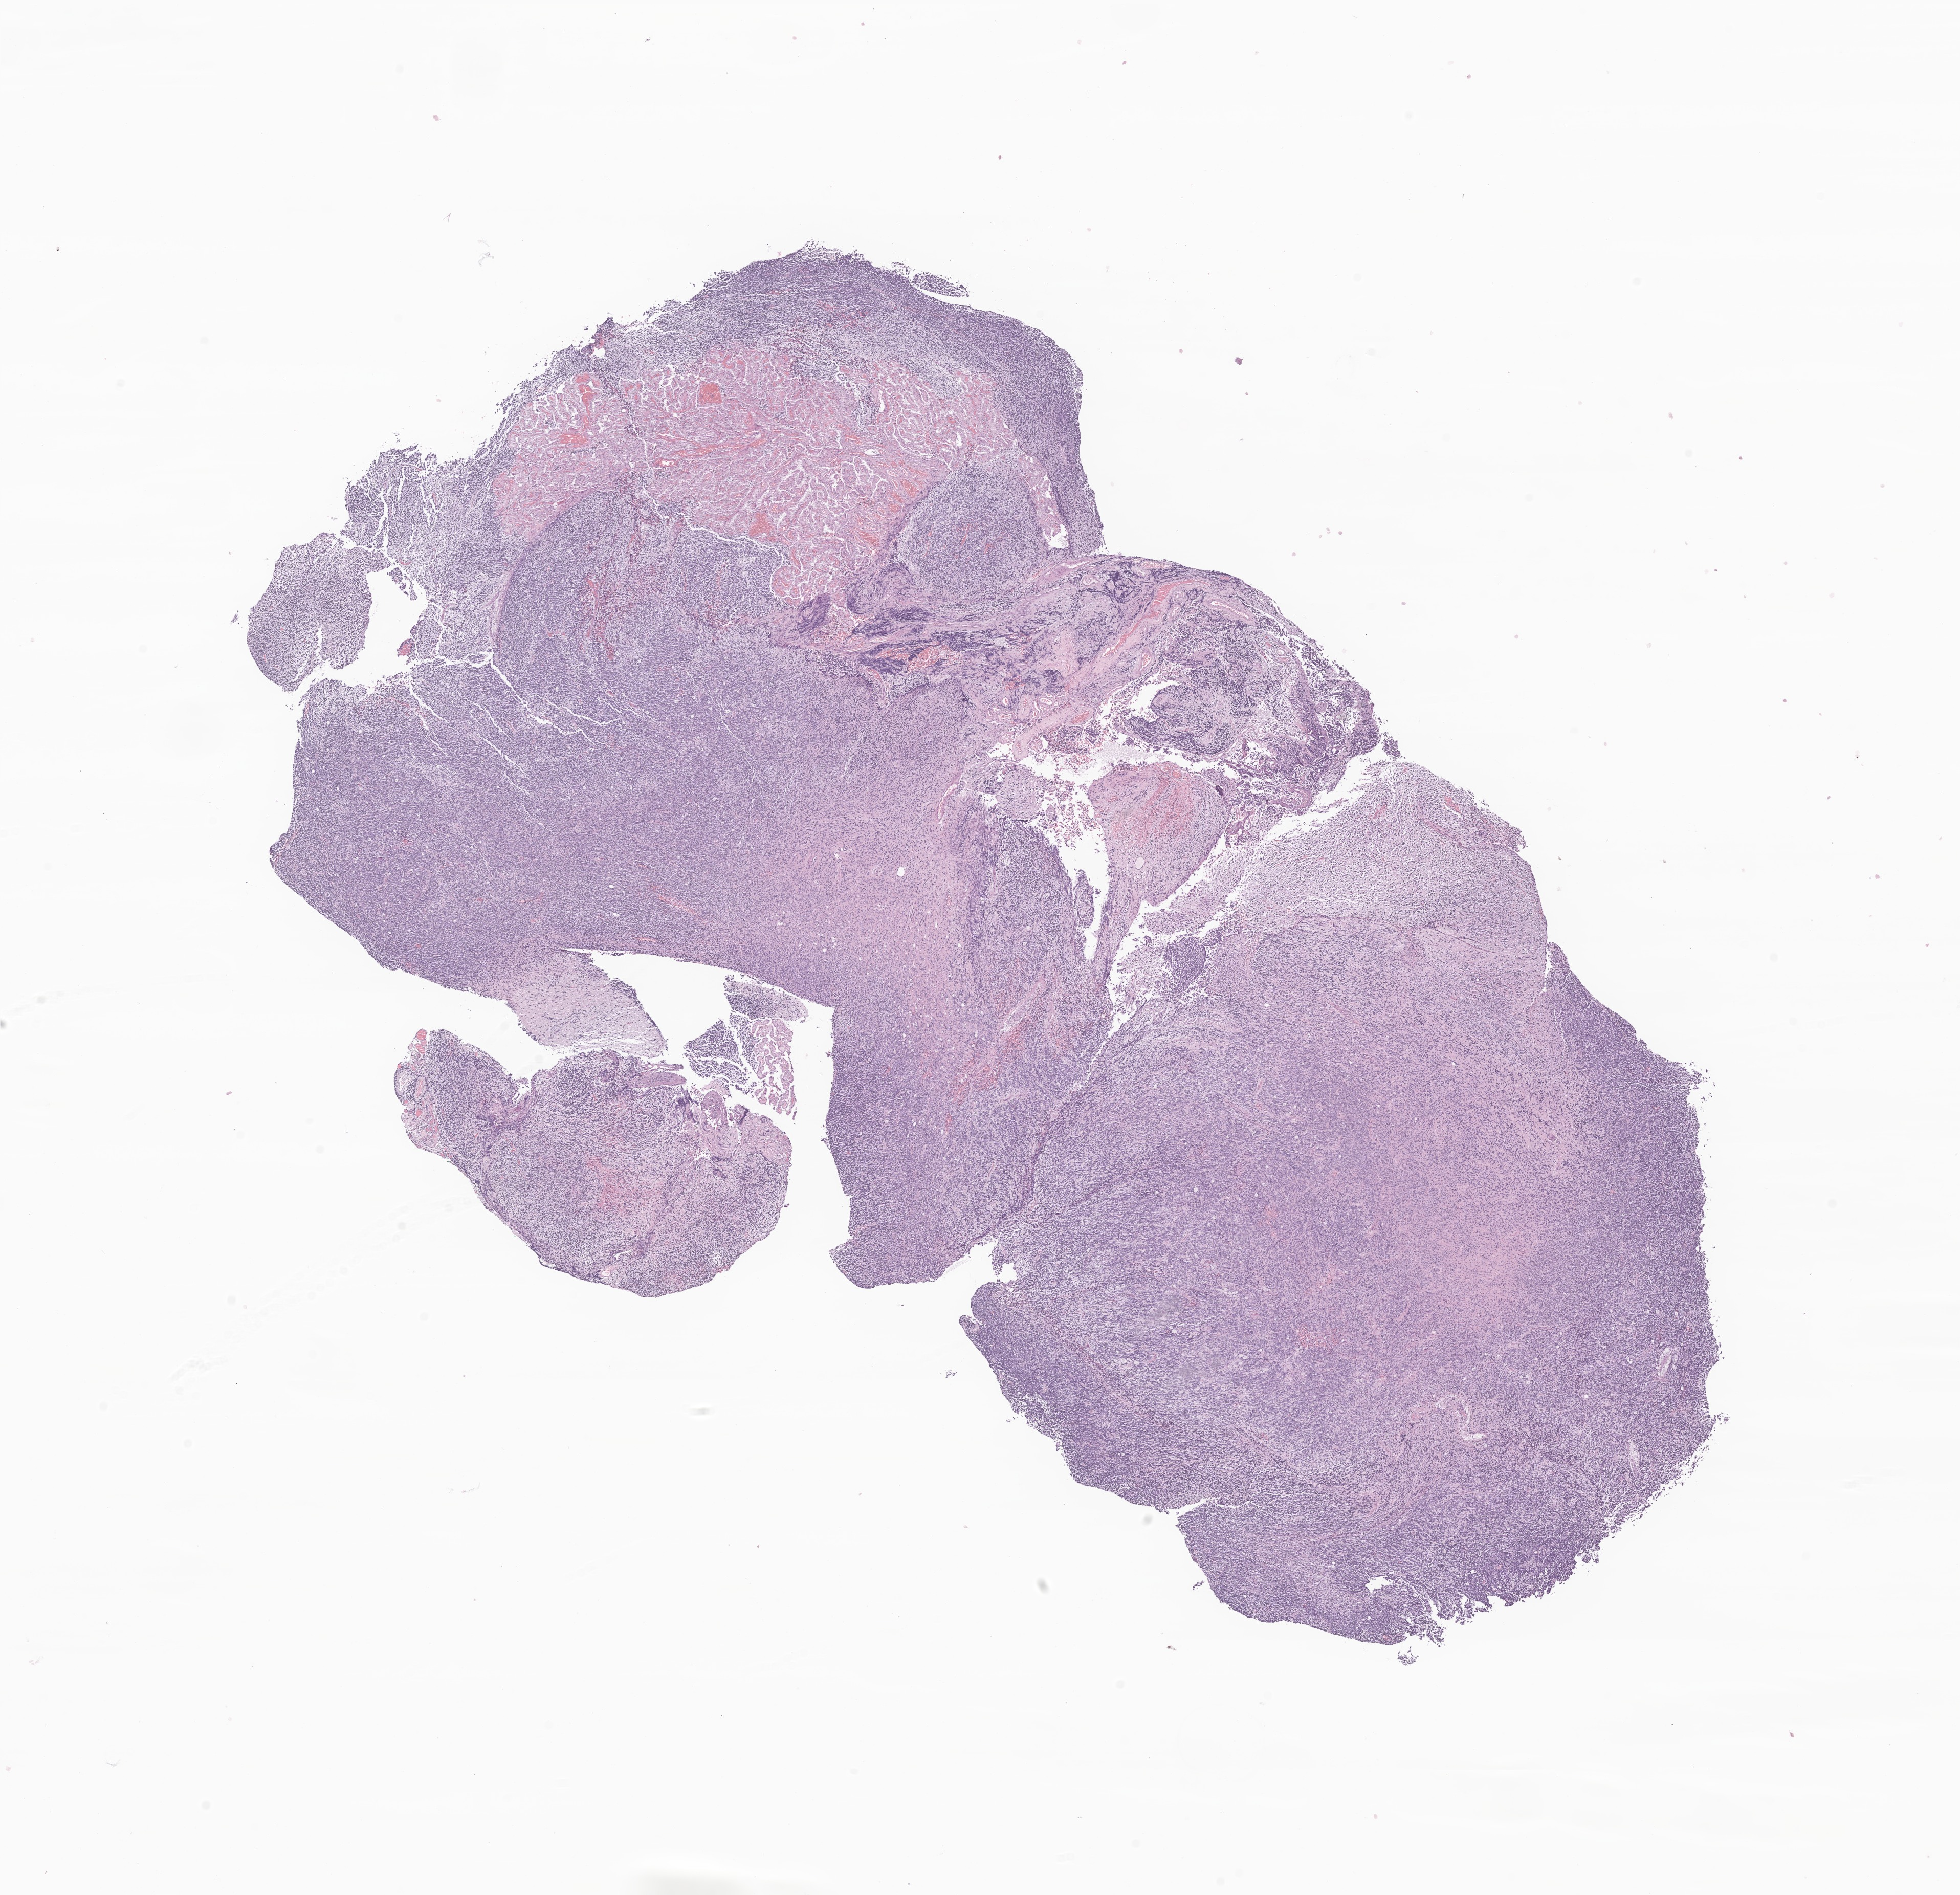
Digitized H&E-stained section of tumor tissue from the brain stem, shown as a low-resolution overview of the whole scanned area (about 16.2 x 15.6 mm); FFPE section. Patient: male, age 264 months.
* diagnosis: Medulloblastoma, NOS